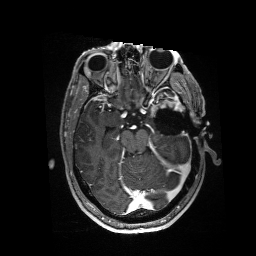
Brain MRI from a brain-tumour surgery series, one axial slice; slice 103 of 176 in the series (ordered by position); T1-weighted post-contrast; 1 mm slice thickness; 256 × 256 image matrix, field of view 256 × 256 mm. From the clinical record (not read from this slice): histopathology: Glioblastoma; WHO grade: 4; IDH mutation: no.
Outlined on this slice (outlined manually by an expert reader):
- residual tumour: bounding box <151,95,185,116> (left, top, right, bottom; pixels)